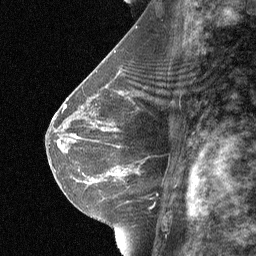
Breast MRI (dynamic contrast-enhanced), one sagittal slice. Position 38 of 64 along the scan axis. Dynamic contrast-enhanced study with each time point stored as its own series, time point 2 of 3 at this slice position (early post-contrast, ordered by acquisition time). 1.5 T. TE 4.8 ms, TR 27 ms. 256 × 256 image matrix. Female patient, age 42 years. Case-level facts recorded for this patient, not image findings: setting: breast cancer imaged before/during neoadjuvant chemotherapy; receptor status: triple-negative.
Structures marked on this image (semi-automatic segmentation, software-assisted and operator-edited):
- analysis volume of interest (the breast-tissue region the enhancement analysis was run in; not a lesion): box from (x=99, y=117) to (x=174, y=187) px
- tumour enhancement mask (voxels above the 90 % enhancement threshold inside the analysis volume of interest): (x=113, y=169)–(x=128, y=174)